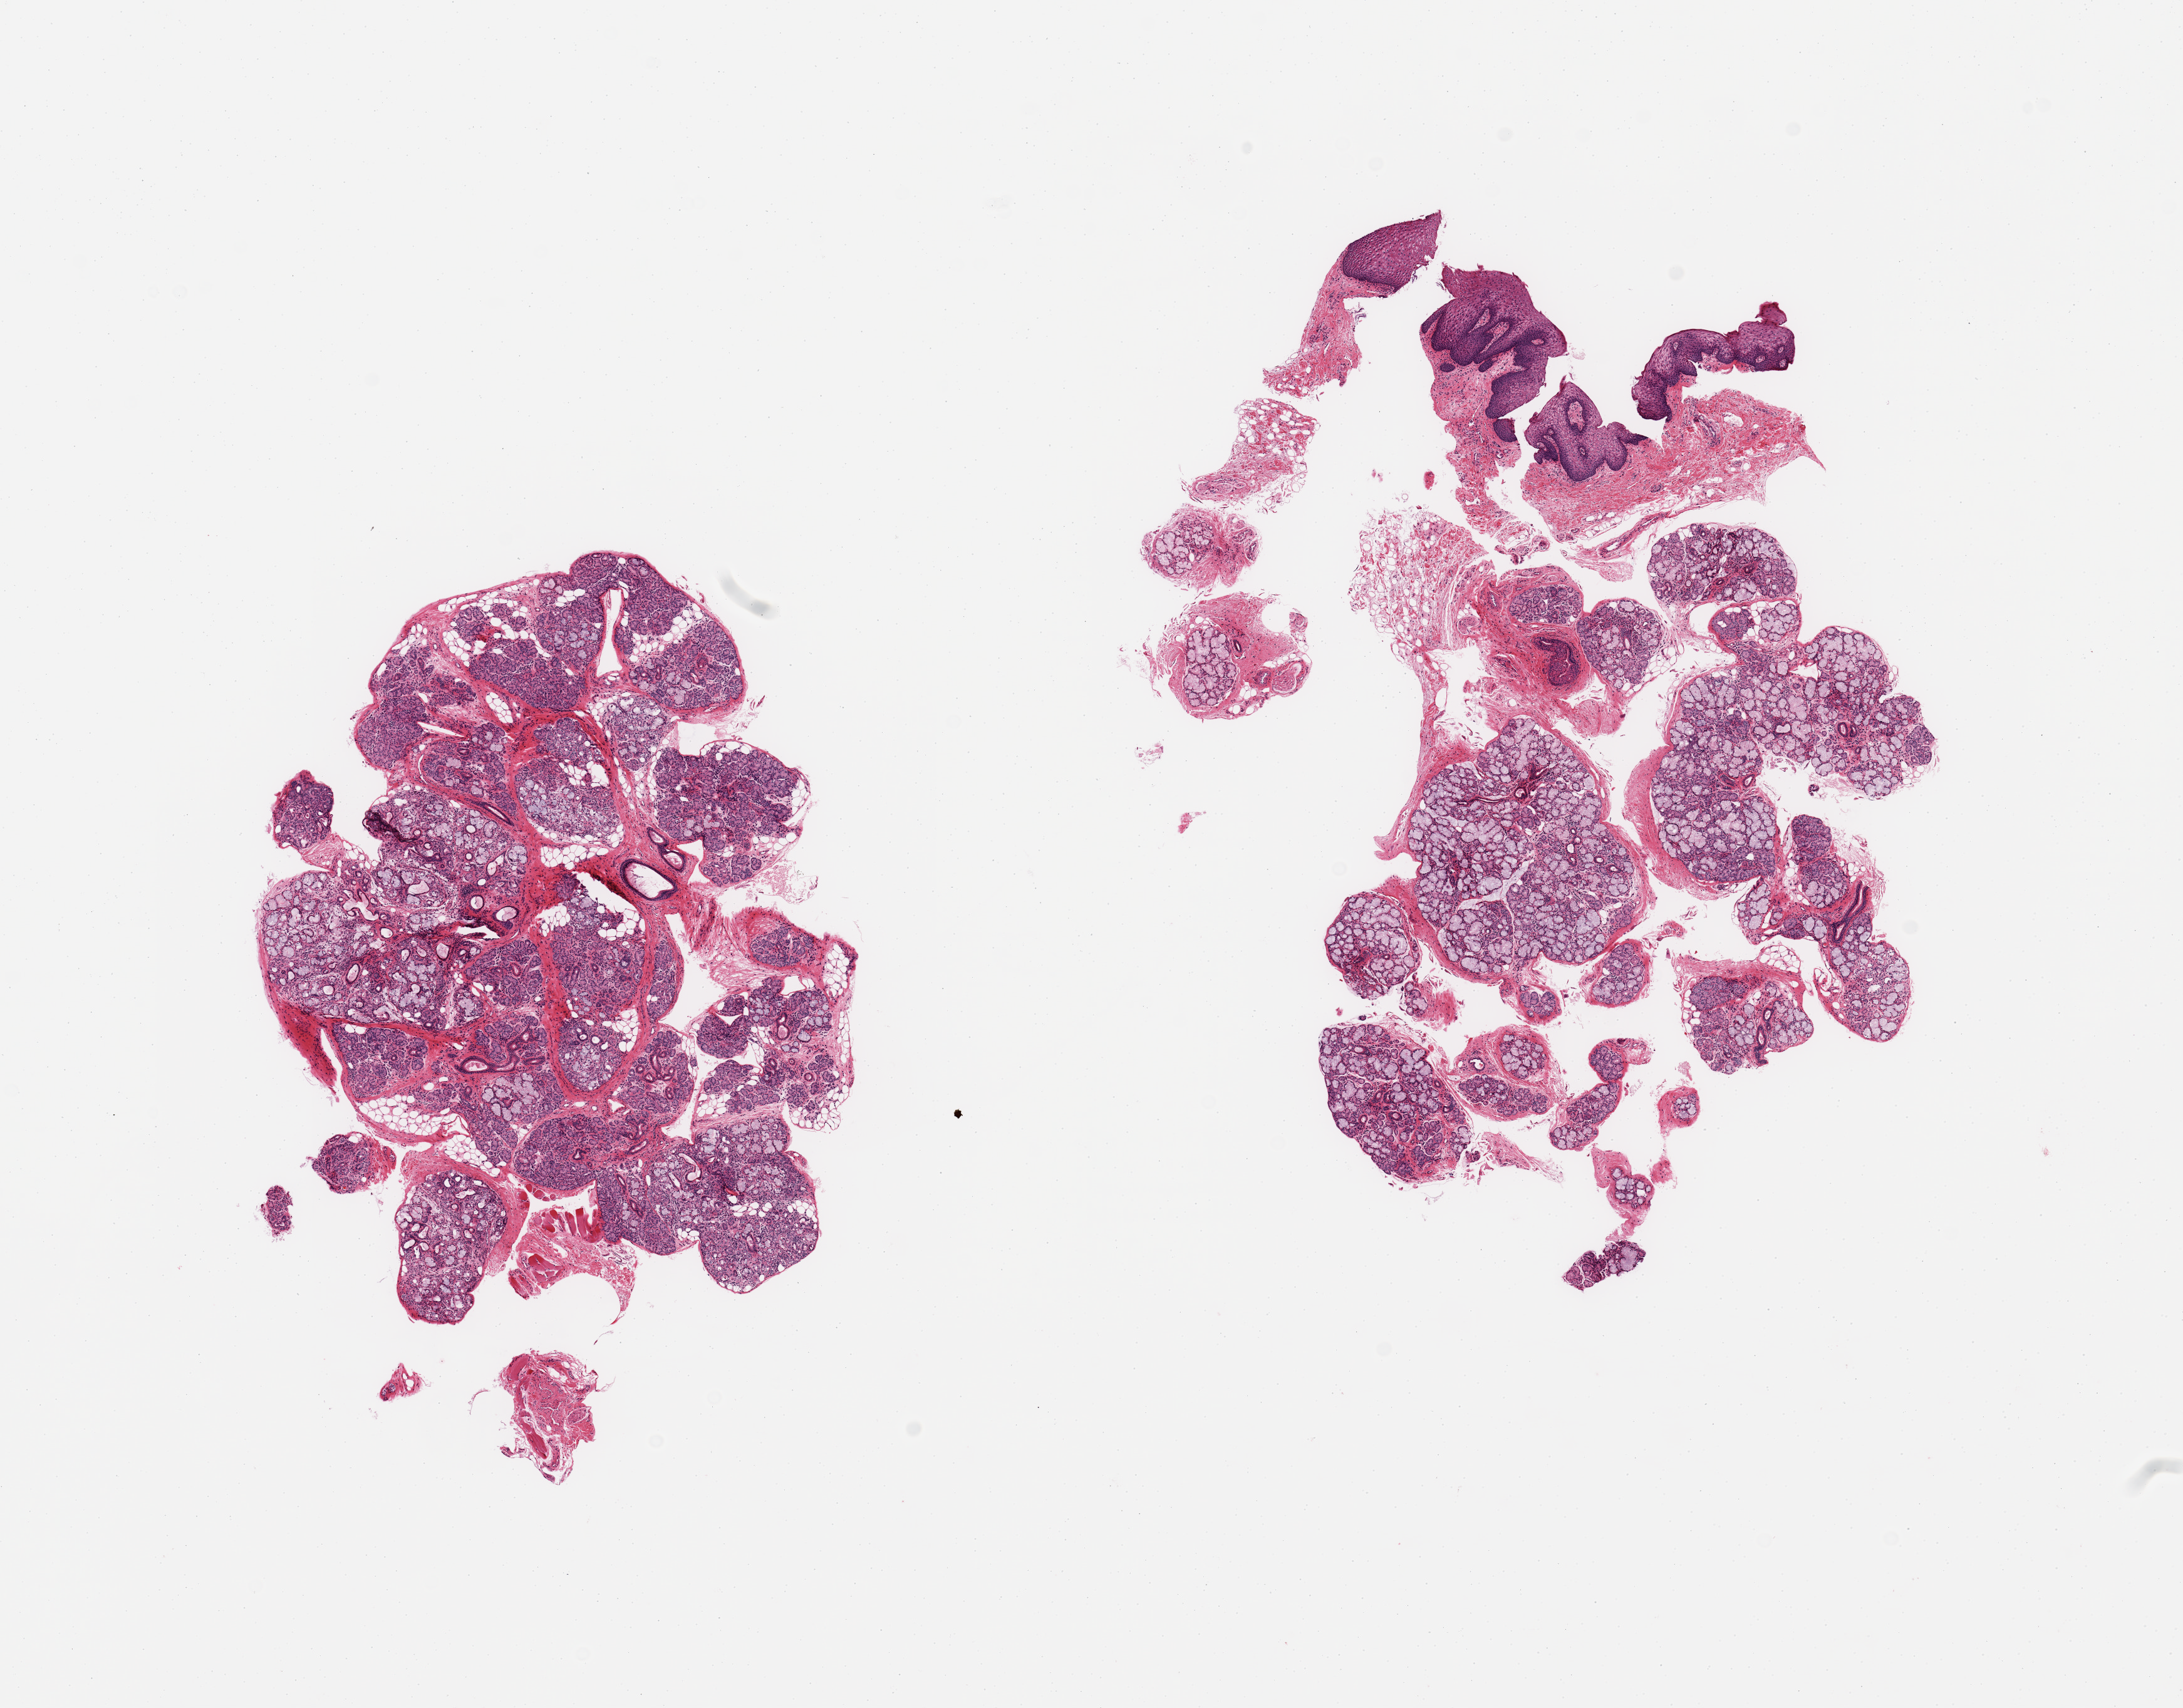
Whole-slide image, haematoxylin and eosin stain — shown as a low-resolution overview of the whole scanned area (about 13.8 x 10.8 mm, slide scanned at 20x), PAXgene-fixed, paraffin-embedded tissue, sampled site (target tissue): minor salivary gland, tissue donor sample.
Review note (as recorded): 2 pieces; 2 glands, 1 with 30% lip at edge.